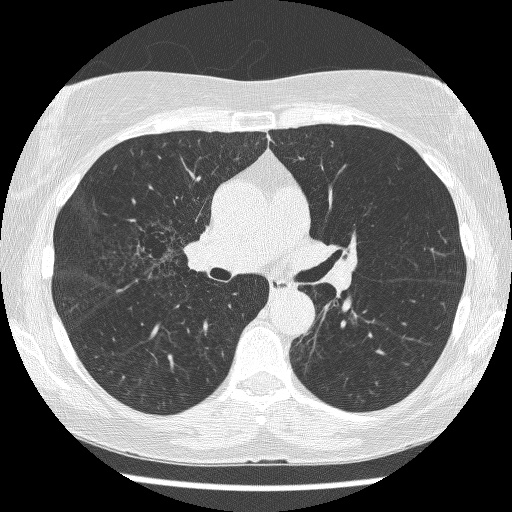
Axial slice from a low-dose chest CT screening exam, baseline screening round, lung window (W 1500 / L -600 HU), 1.25 mm slice thickness, lung (sharp) reconstruction kernel (BONE), slice 163 of 271 in the series. Female, age 64 years at enrolment.
Lesion marked by an expert reader, box from (x=122, y=214) to (x=198, y=274) px. The screening reader recorded 3 non-calcified nodules or masses ≥4 mm on this exam; which of them this box marks is not recorded. Participant outcome: lung cancer diagnosed 735 days after this screen — adenocarcinoma, NOS, right upper lobe, right middle lobe, right hilum, stage IV (AJCC 6th edition), 85 mm at pathology.